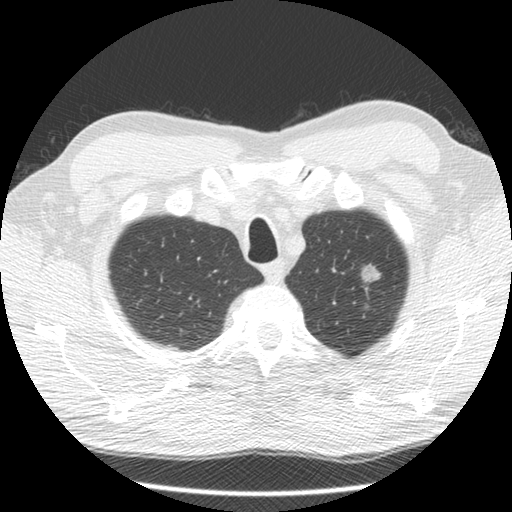
Low-dose screening chest CT, one axial slice; slice 118 of 132 in the series (ordered by position); 120 kVp; lung window (W 1500 / L -600 HU); 512 × 512 image matrix.
Structures marked on this image (outlined manually by an expert reader):
- lesion 1 (tumor, upper lobe of left lung): bounding box <361,263,381,283> (left, top, right, bottom; pixels)